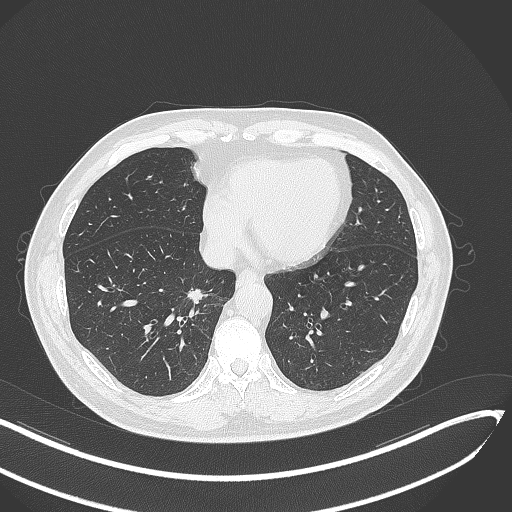
Chest CT, one axial slice. Position 123 of 429 along the scan axis. Reconstruction kernel B70f. 120 kVp. Lung window (W 1500 / L -600 HU). 1 mm slice thickness. 512 × 512 image matrix, field of view 400 × 400 mm. Male patient, age 62 years. From the clinical record (not read from this slice): clinical TNM (as recorded): T1b N0 M0.
Structures marked on this image (rectangle marked by the reading radiologist):
- lung tumour (recorded histology: adenocarcinoma): bounding box [x1, y1, x2, y2] px = [183, 286, 208, 307]